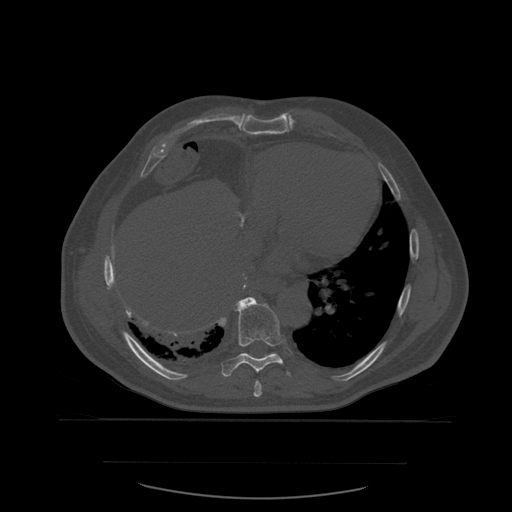
CT including the spine, one axial slice; slice 339 of 590 in the series (ordered by position); bone window (W 1800 / L 400 HU); 512 × 512 image matrix, field of view 479 × 479 mm. Patient age 71 years. From the clinical record (not read from this slice): primary cancer: lung.
Annotated regions visible in this slice (semi-automatically segmented with operator editing):
- T8 vertebra: bounding box <254,381,262,398> (left, top, right, bottom; pixels)
- T9 vertebra: <221,297,291,377>